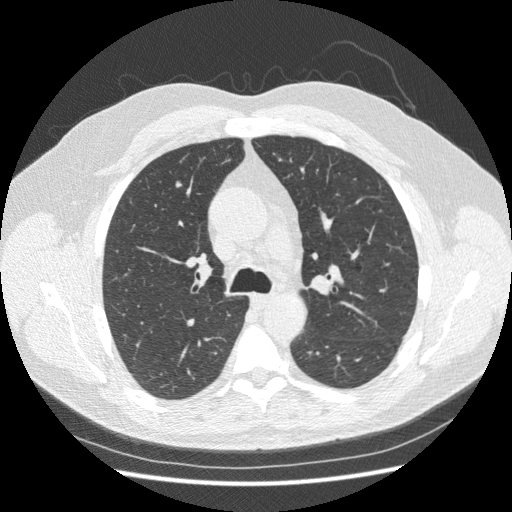
Axial slice from a low-dose chest CT screening exam, baseline annual screen, lung window (W 1500 / L -600 HU), 1.25 mm slice thickness, slice 91 of 250 in the series. Male participant, aged 63 years at enrolment. Current smoker at enrolment.
- Lesion marked by an expert reader, bounding box <168,176,187,193> (left, top, right, bottom; pixels).
- Reader record for this screening exam (exam-level; its link to the box is not recorded): non-calcified nodule or mass ≥4 mm, right upper lobe, 5 × 4 mm, smooth margins, soft tissue attenuation.
- Later outcome: lung cancer diagnosed 202 days after this screen — large cell carcinoma, NOS, right upper lobe, poorly differentiated (G3), stage IIIA (AJCC 6th edition), 15 mm at pathology.